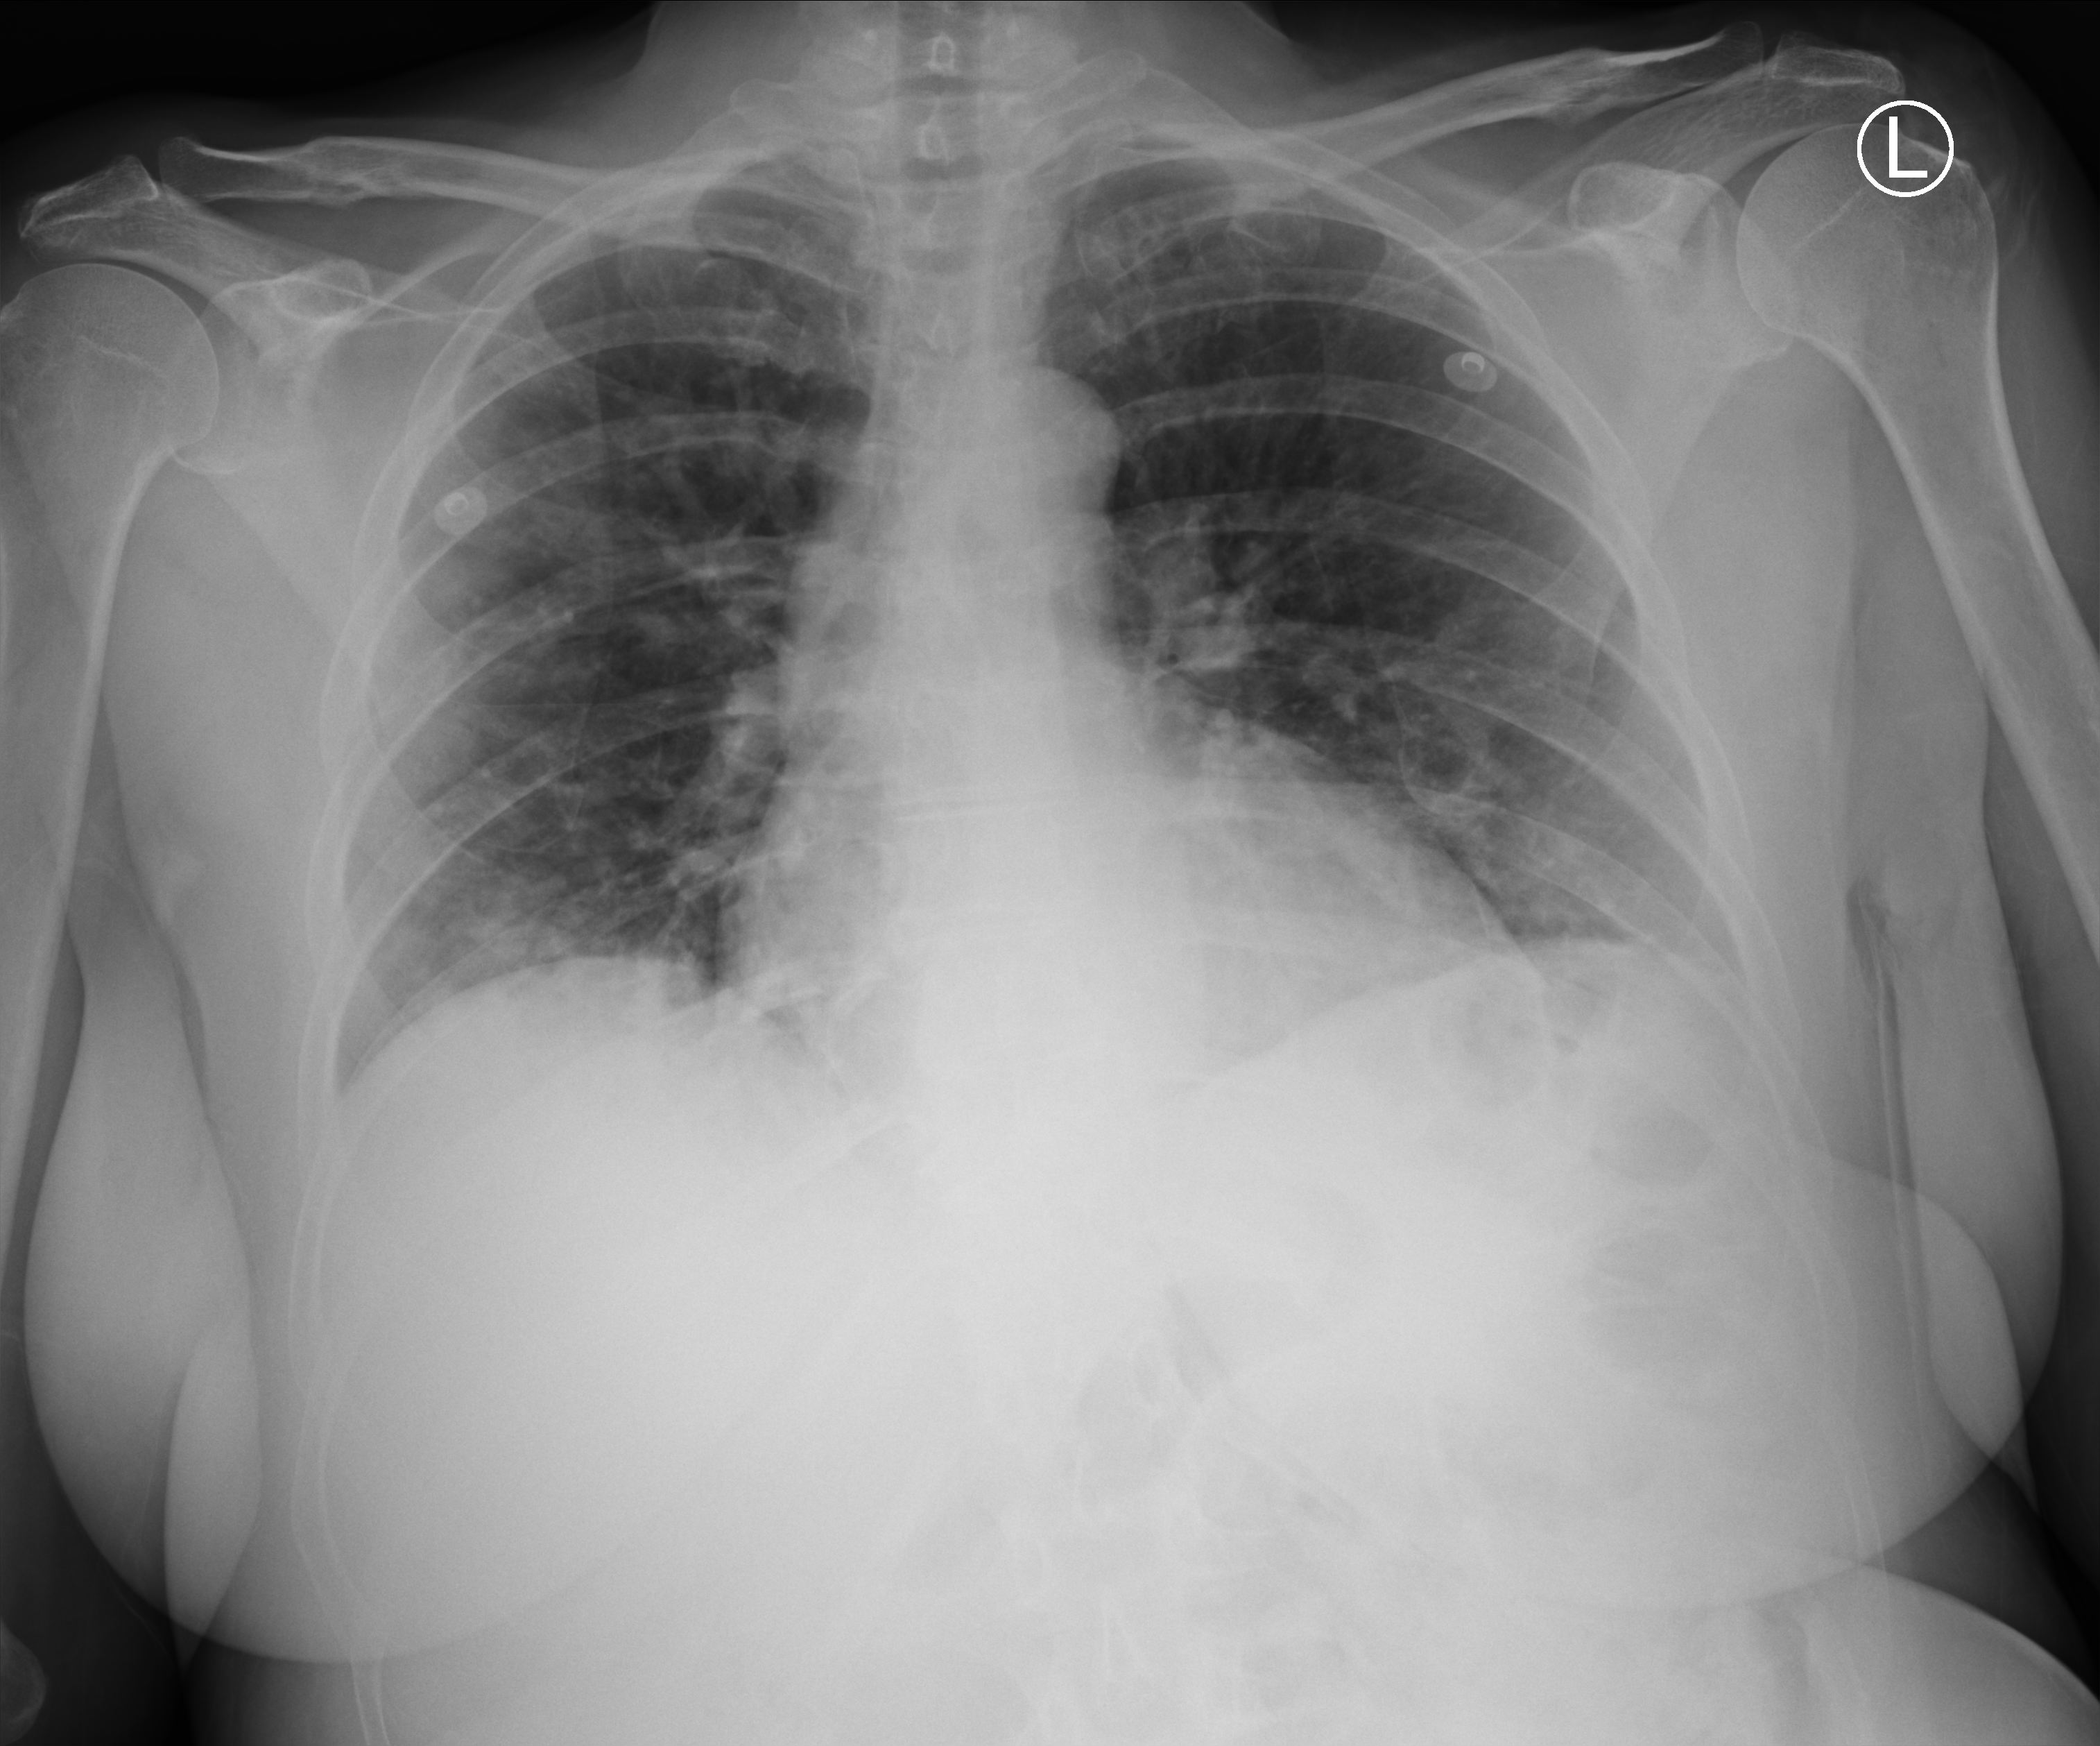
Bedside chest radiograph (computed radiography), anteroposterior (AP) projection. Patient hospitalised with COVID-19; female, aged 18–59 years.
From the hospital-stay record, not from the radiograph (when in the stay this image was taken is not recorded): hypertension (admission record): no; length of hospital stay: 3 days; chronic kidney disease (admission record): no.